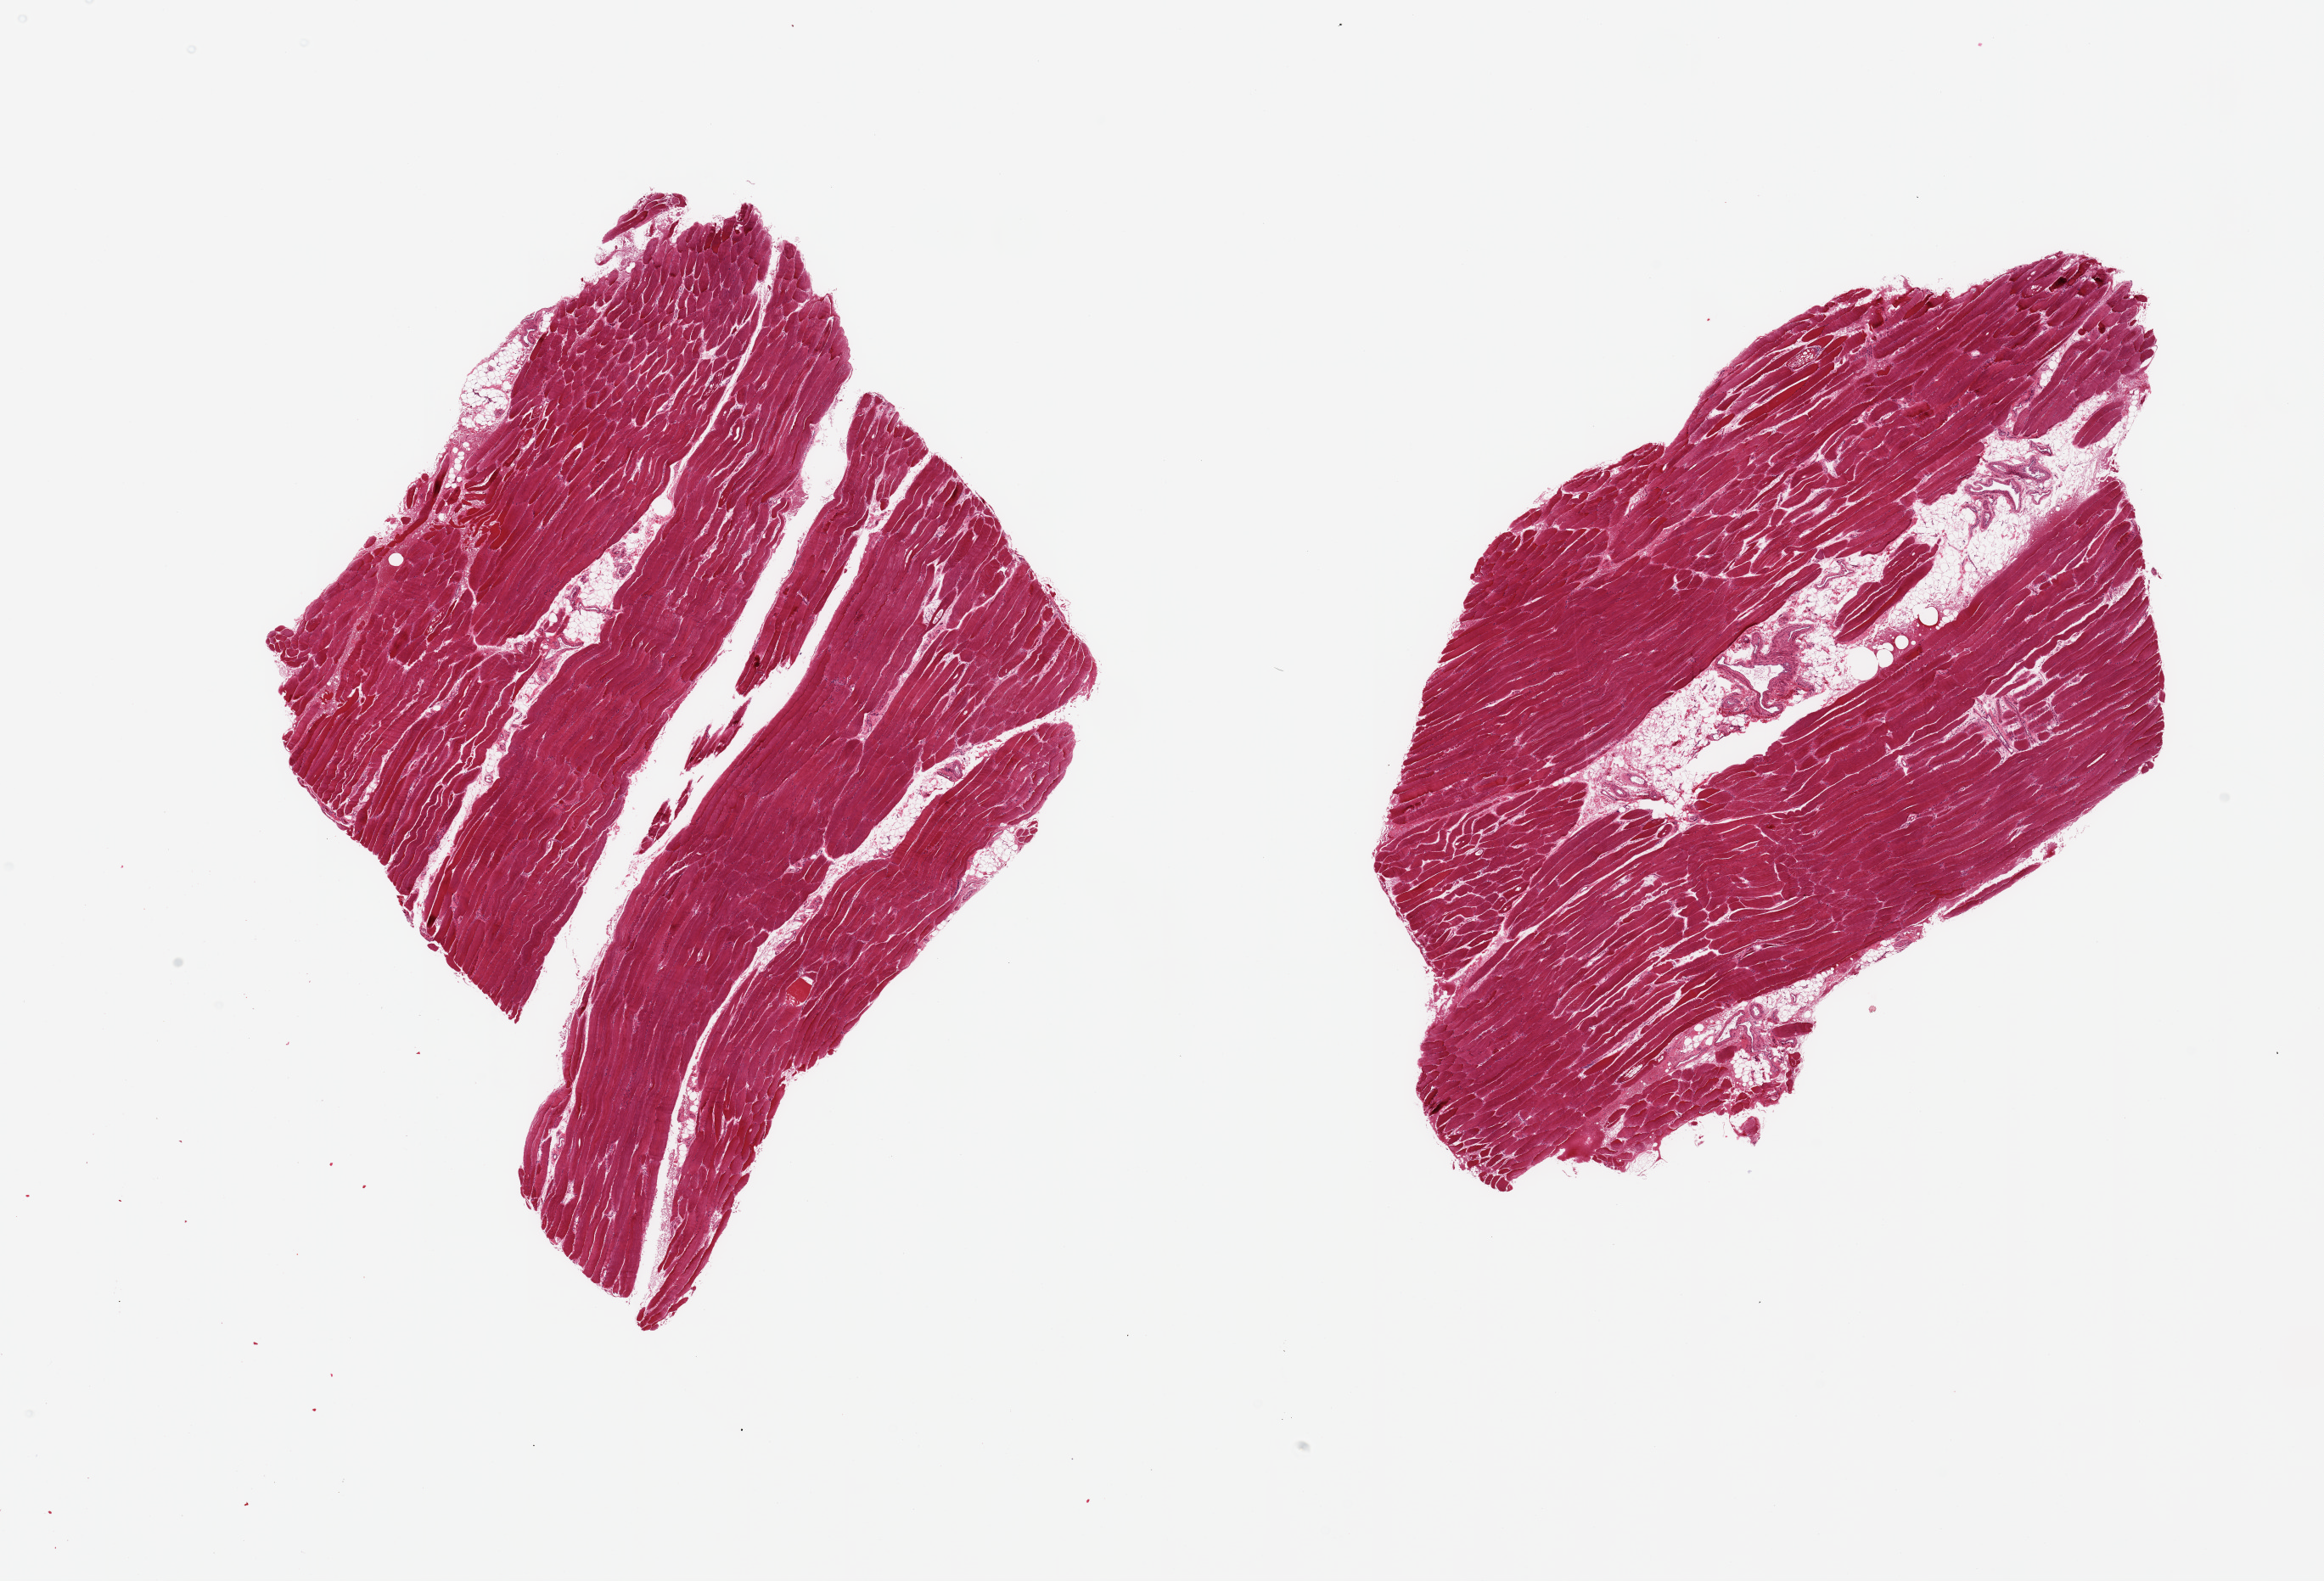
Digitized haematoxylin and eosin-stained section, shown as a low-resolution overview of the whole scanned area (about 21.7 x 14.7 mm). PAXgene-fixed, paraffin-embedded tissue. Section of skeletal muscle (target tissue). Donor tissue sample.
Reviewer comment on this tissue sample: 2 pieces, ~10% interstitial fat/vascular elements.